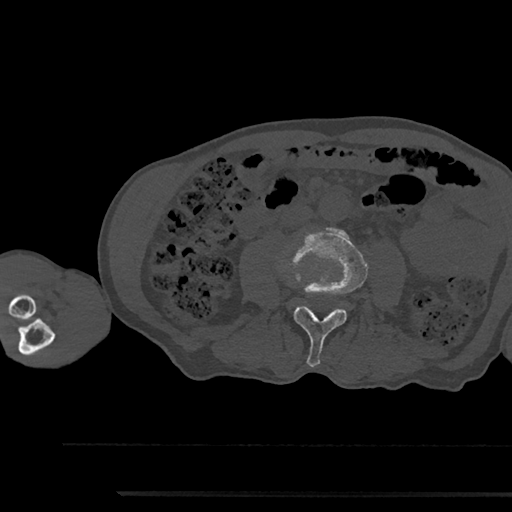
CT including the spine, one axial slice; position 466 of 797 along the scan axis; 120 kVp; bone window (W 1800 / L 400 HU); 0.5 mm slice thickness; 512 × 512 image matrix, field of view 367 × 367 mm. Patient: male, 79 years. From the clinical record (not read from this slice): primary cancer: prostate.
Annotated regions visible in this slice (semi-automatically segmented with operator editing):
- L3 vertebra: bounding box <282,228,368,367> (left, top, right, bottom; pixels)